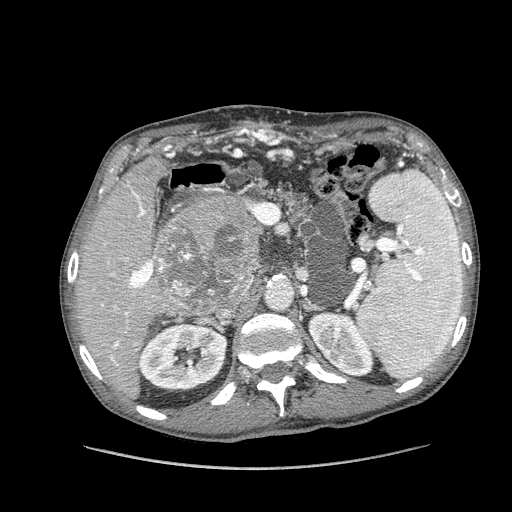
Contrast-enhanced abdominal CT (liver protocol), one axial slice. 100 kVp. Soft-tissue window (W 400 / L 40 HU). 2.5 mm slice thickness. 512 × 512 image matrix, field of view 400 × 400 mm. From the clinical record (not read from this slice): diagnosis: hepatocellular carcinoma (patient treated with transarterial chemoembolisation; whether this scan precedes or follows treatment is not stated here); TNM stage (as recorded): Stage-IIIA; Child-Pugh class: A; tumour nodularity: multinodular.
Structures marked on this image (semi-automatically segmented with operator editing):
- liver parenchyma outside the tumour (the mass and vessels are separate outlines, so this box may not span the whole liver): bounding box [x1, y1, x2, y2] px = [76, 156, 226, 398]
- mass: [152, 196, 260, 314]
- liver vessels: [102, 190, 154, 361]